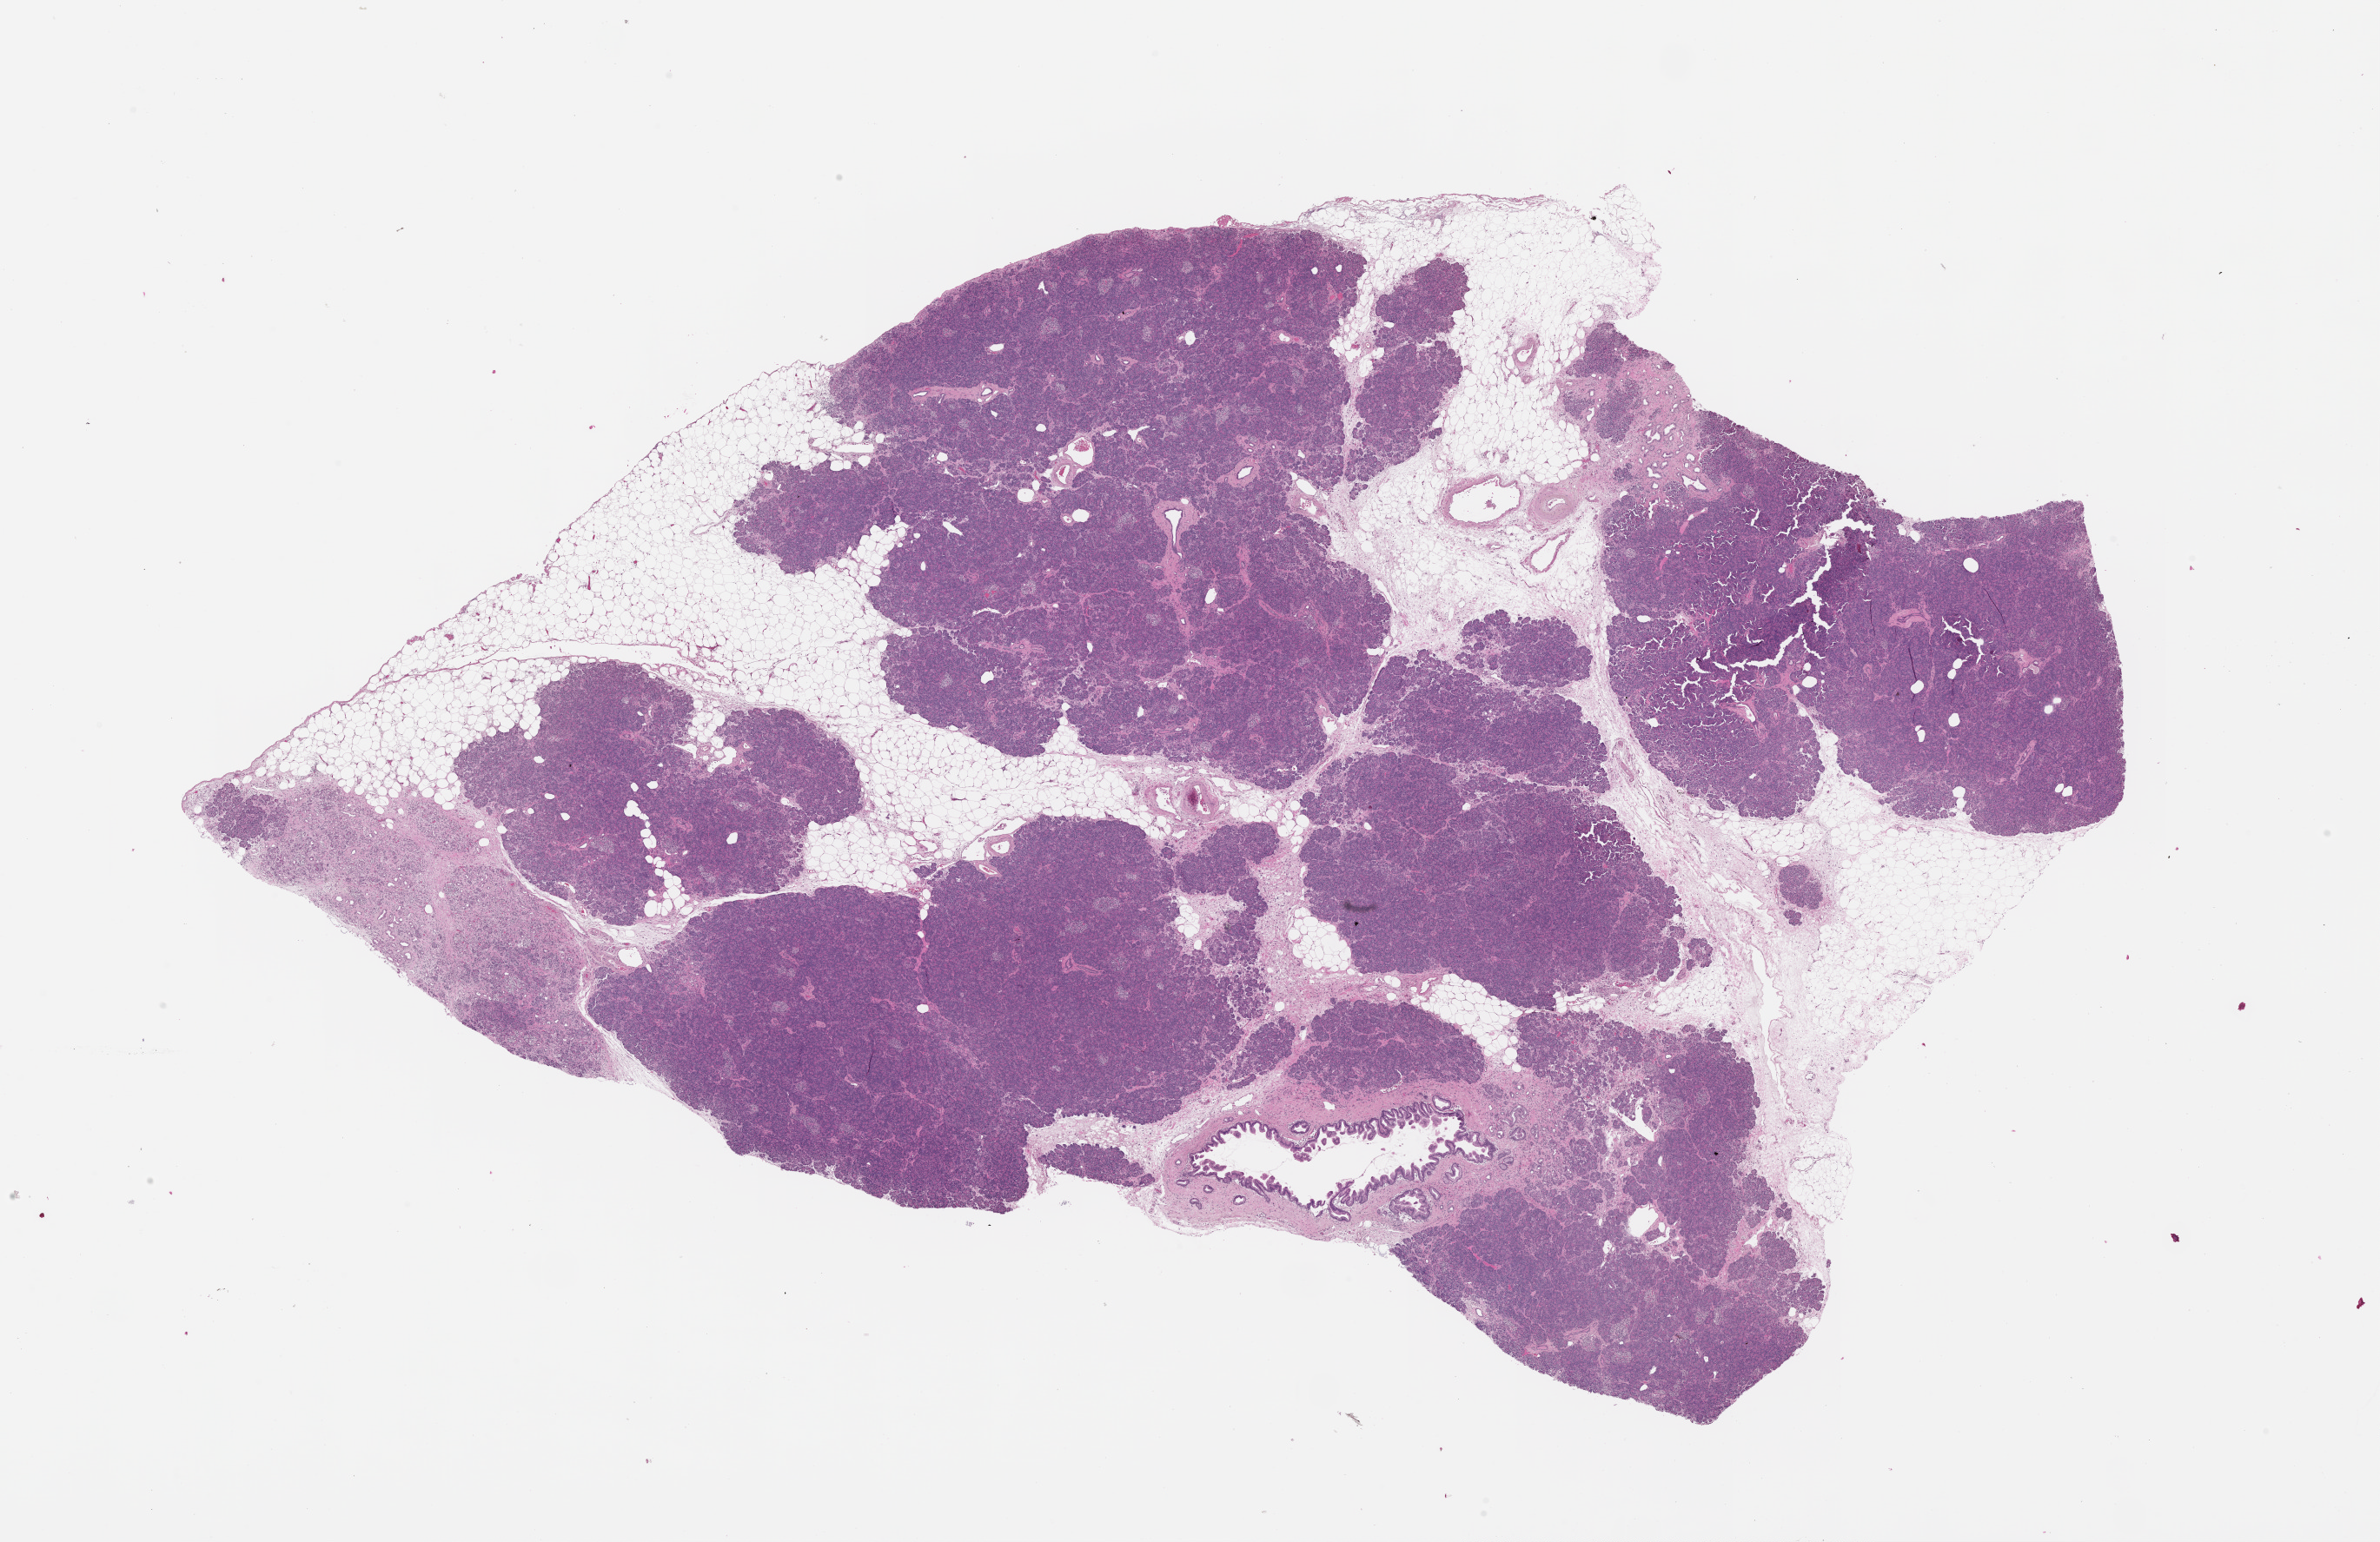
Digitized Hematoxylin and eosin (H&E) stained tissue section (whole slide) — whole scanned area (about 22.0 x 14.3 mm, from a 20x scan) shown as a low-resolution overview; normal (non-tumour) tissue sample, sampled site: pancreas. Male, 78 y/o.
• this section: normal (non-tumour) tissue from the same patient
• patient diagnosis: Infiltrating duct carcinoma, NOS